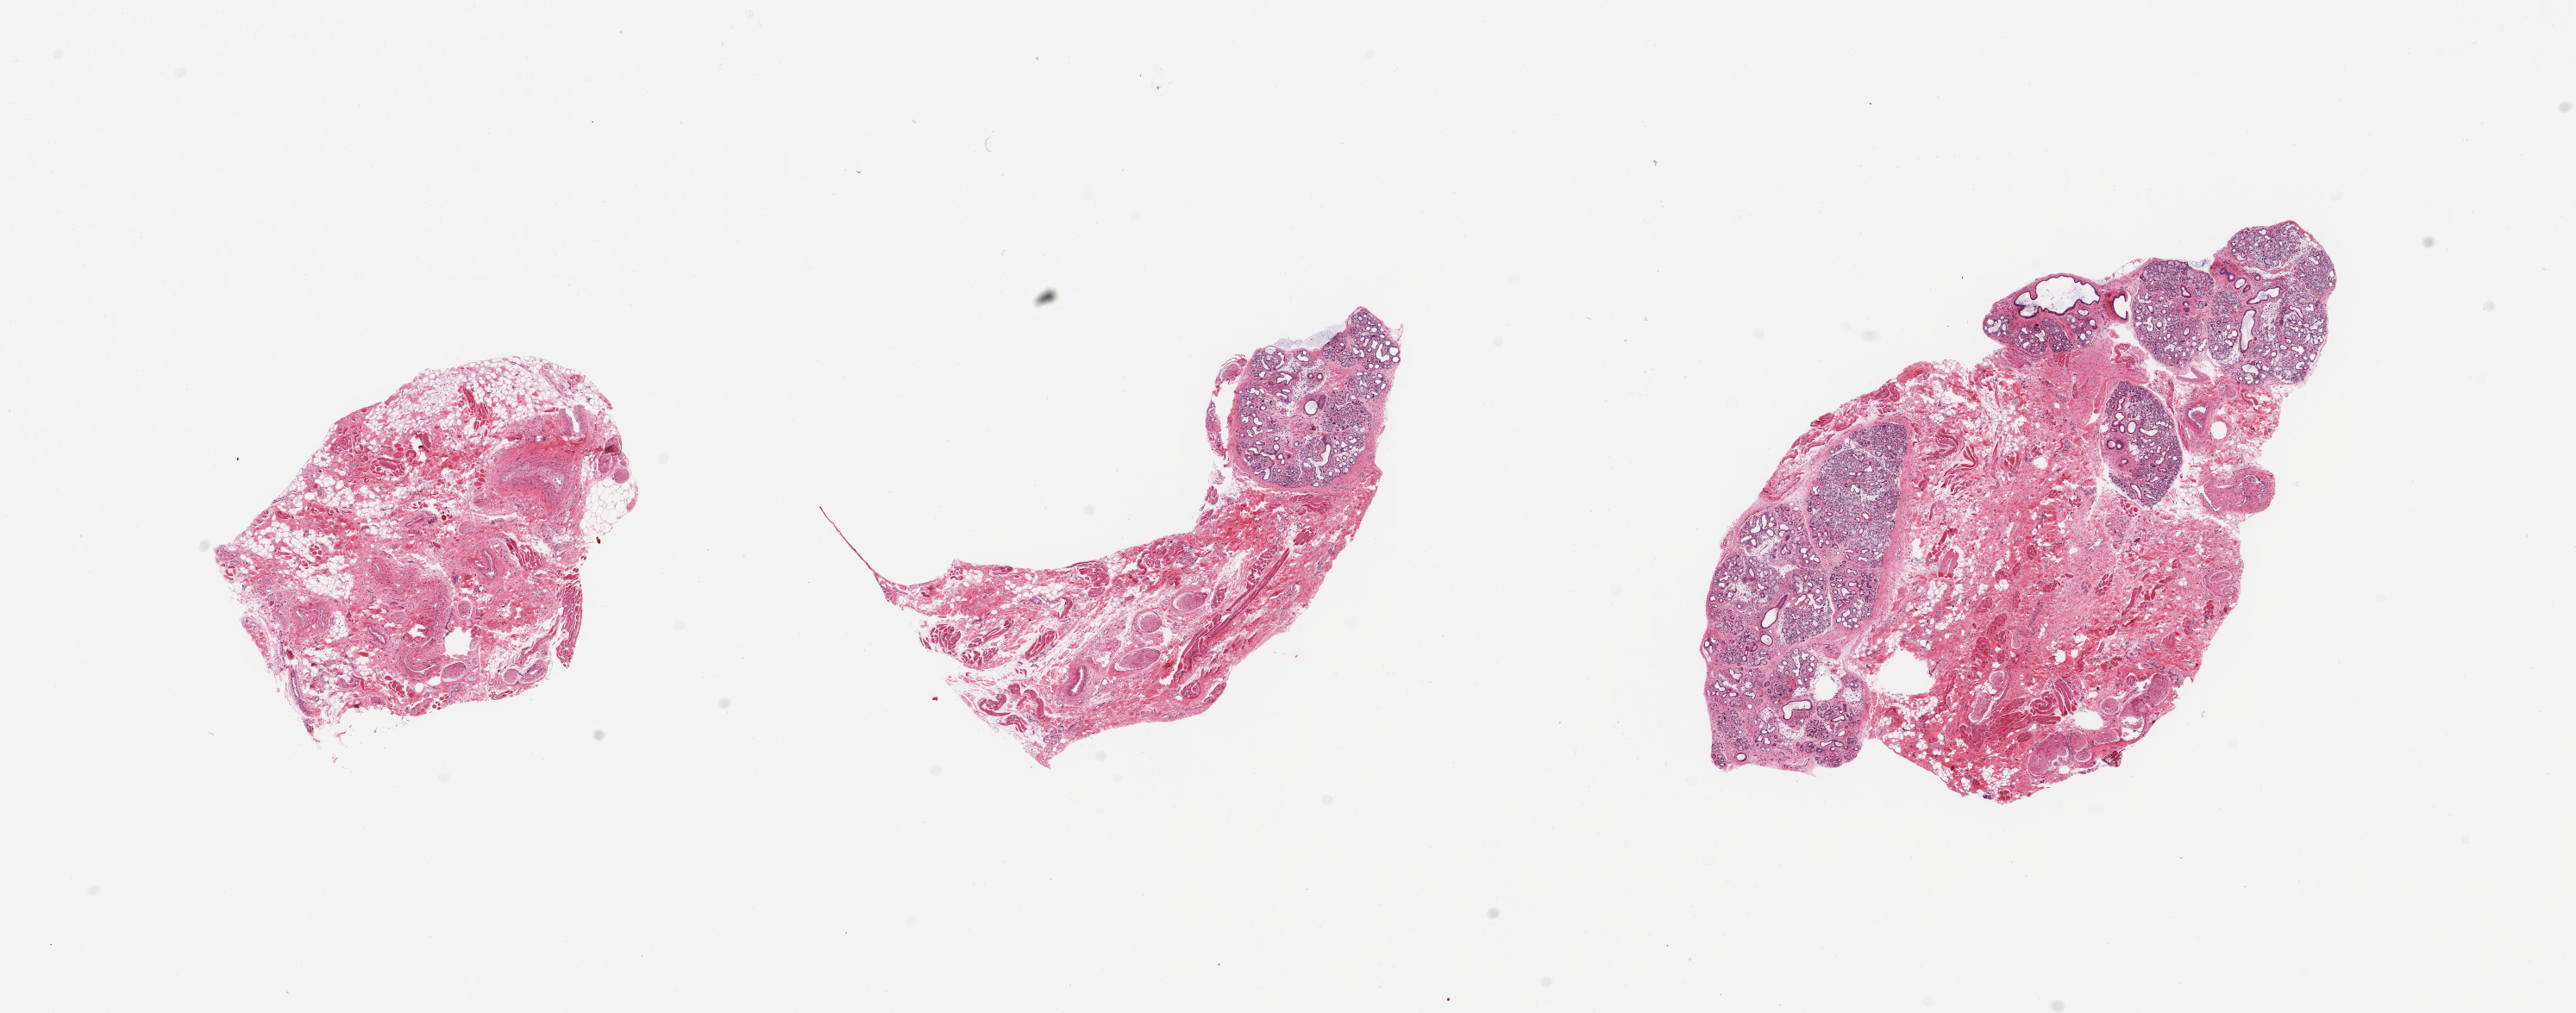
H&E whole-slide image, brightfield, low-resolution overview of the scanned area, about 23.6 x 9.3 mm, PAXgene-fixed, paraffin-embedded tissue, section of minor salivary gland (target tissue), donor tissue sample.
Pathologist's review note for this sample: 3 pieces; 0, 20, and 40% salivary gland elements, remainder is fat, nerve, skeletal muscle, and vessels.